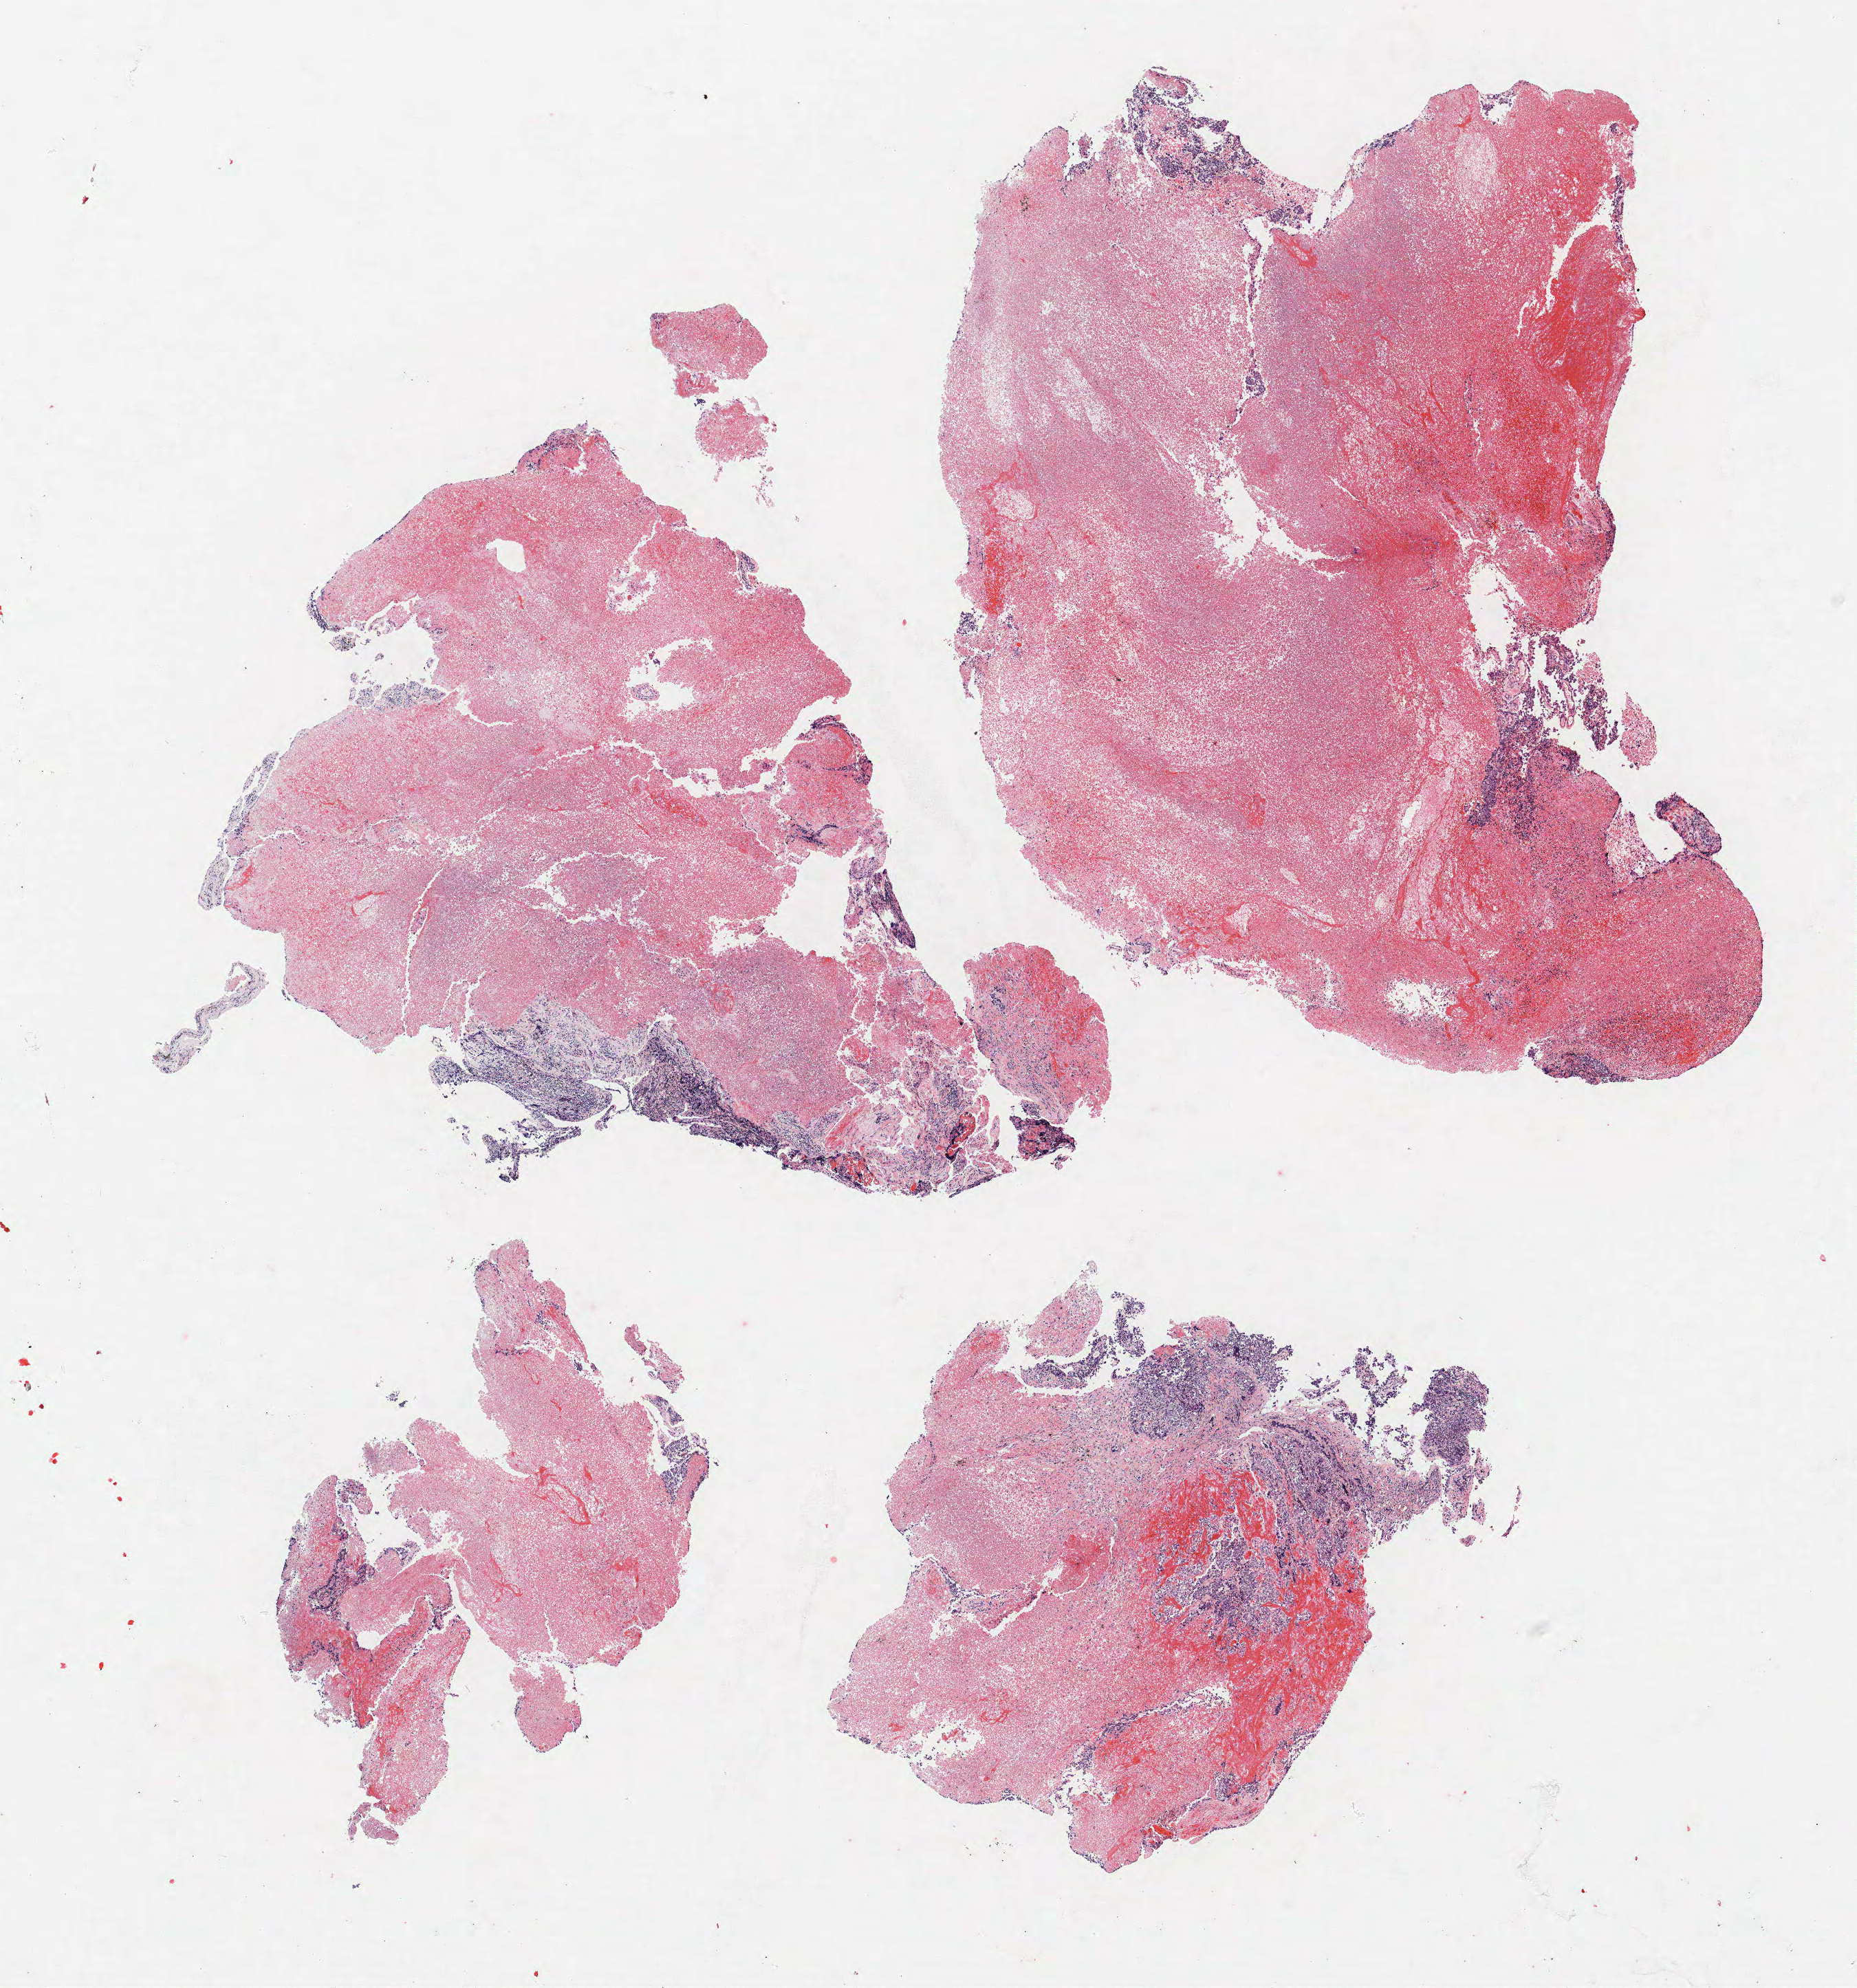
Hematoxylin and eosin (H&E) stained whole-slide image — shown as a low-resolution overview of the whole scanned area (about 10.8 x 11.6 mm), formalin-fixed paraffin-embedded (FFPE) section, lung tissue. Male patient, aged 62 at enrolment. Grade: poorly differentiated (G3).
ICD-O-3 topography: lung, NOS (C34.9). Participant's lung-cancer diagnosis: Squamous cell carcinoma, NOS (ICD-O-3 8070/3). Stage (AJCC 6th edition): IV.